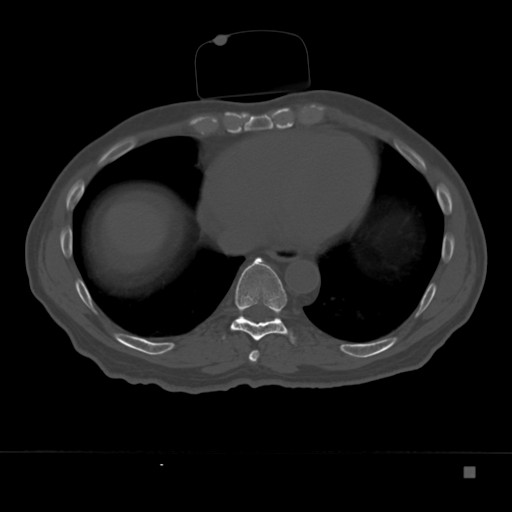
CT including the spine, one axial slice. Slice 189 of 332 in the series (ordered by position). 120 kVp. Bone window (W 1800 / L 400 HU). 1.5 mm slice thickness. 512 × 512 image matrix, field of view 389 × 389 mm. Male patient, age 72 years. Case-level facts recorded for this patient, not image findings: primary cancer: skeletal.
Annotated regions visible in this slice (semi-automatic segmentation, software-assisted and operator-edited):
- T8 vertebra: bounding box <248,350,260,362> (left, top, right, bottom; pixels)
- T9 vertebra: <223,257,295,344>